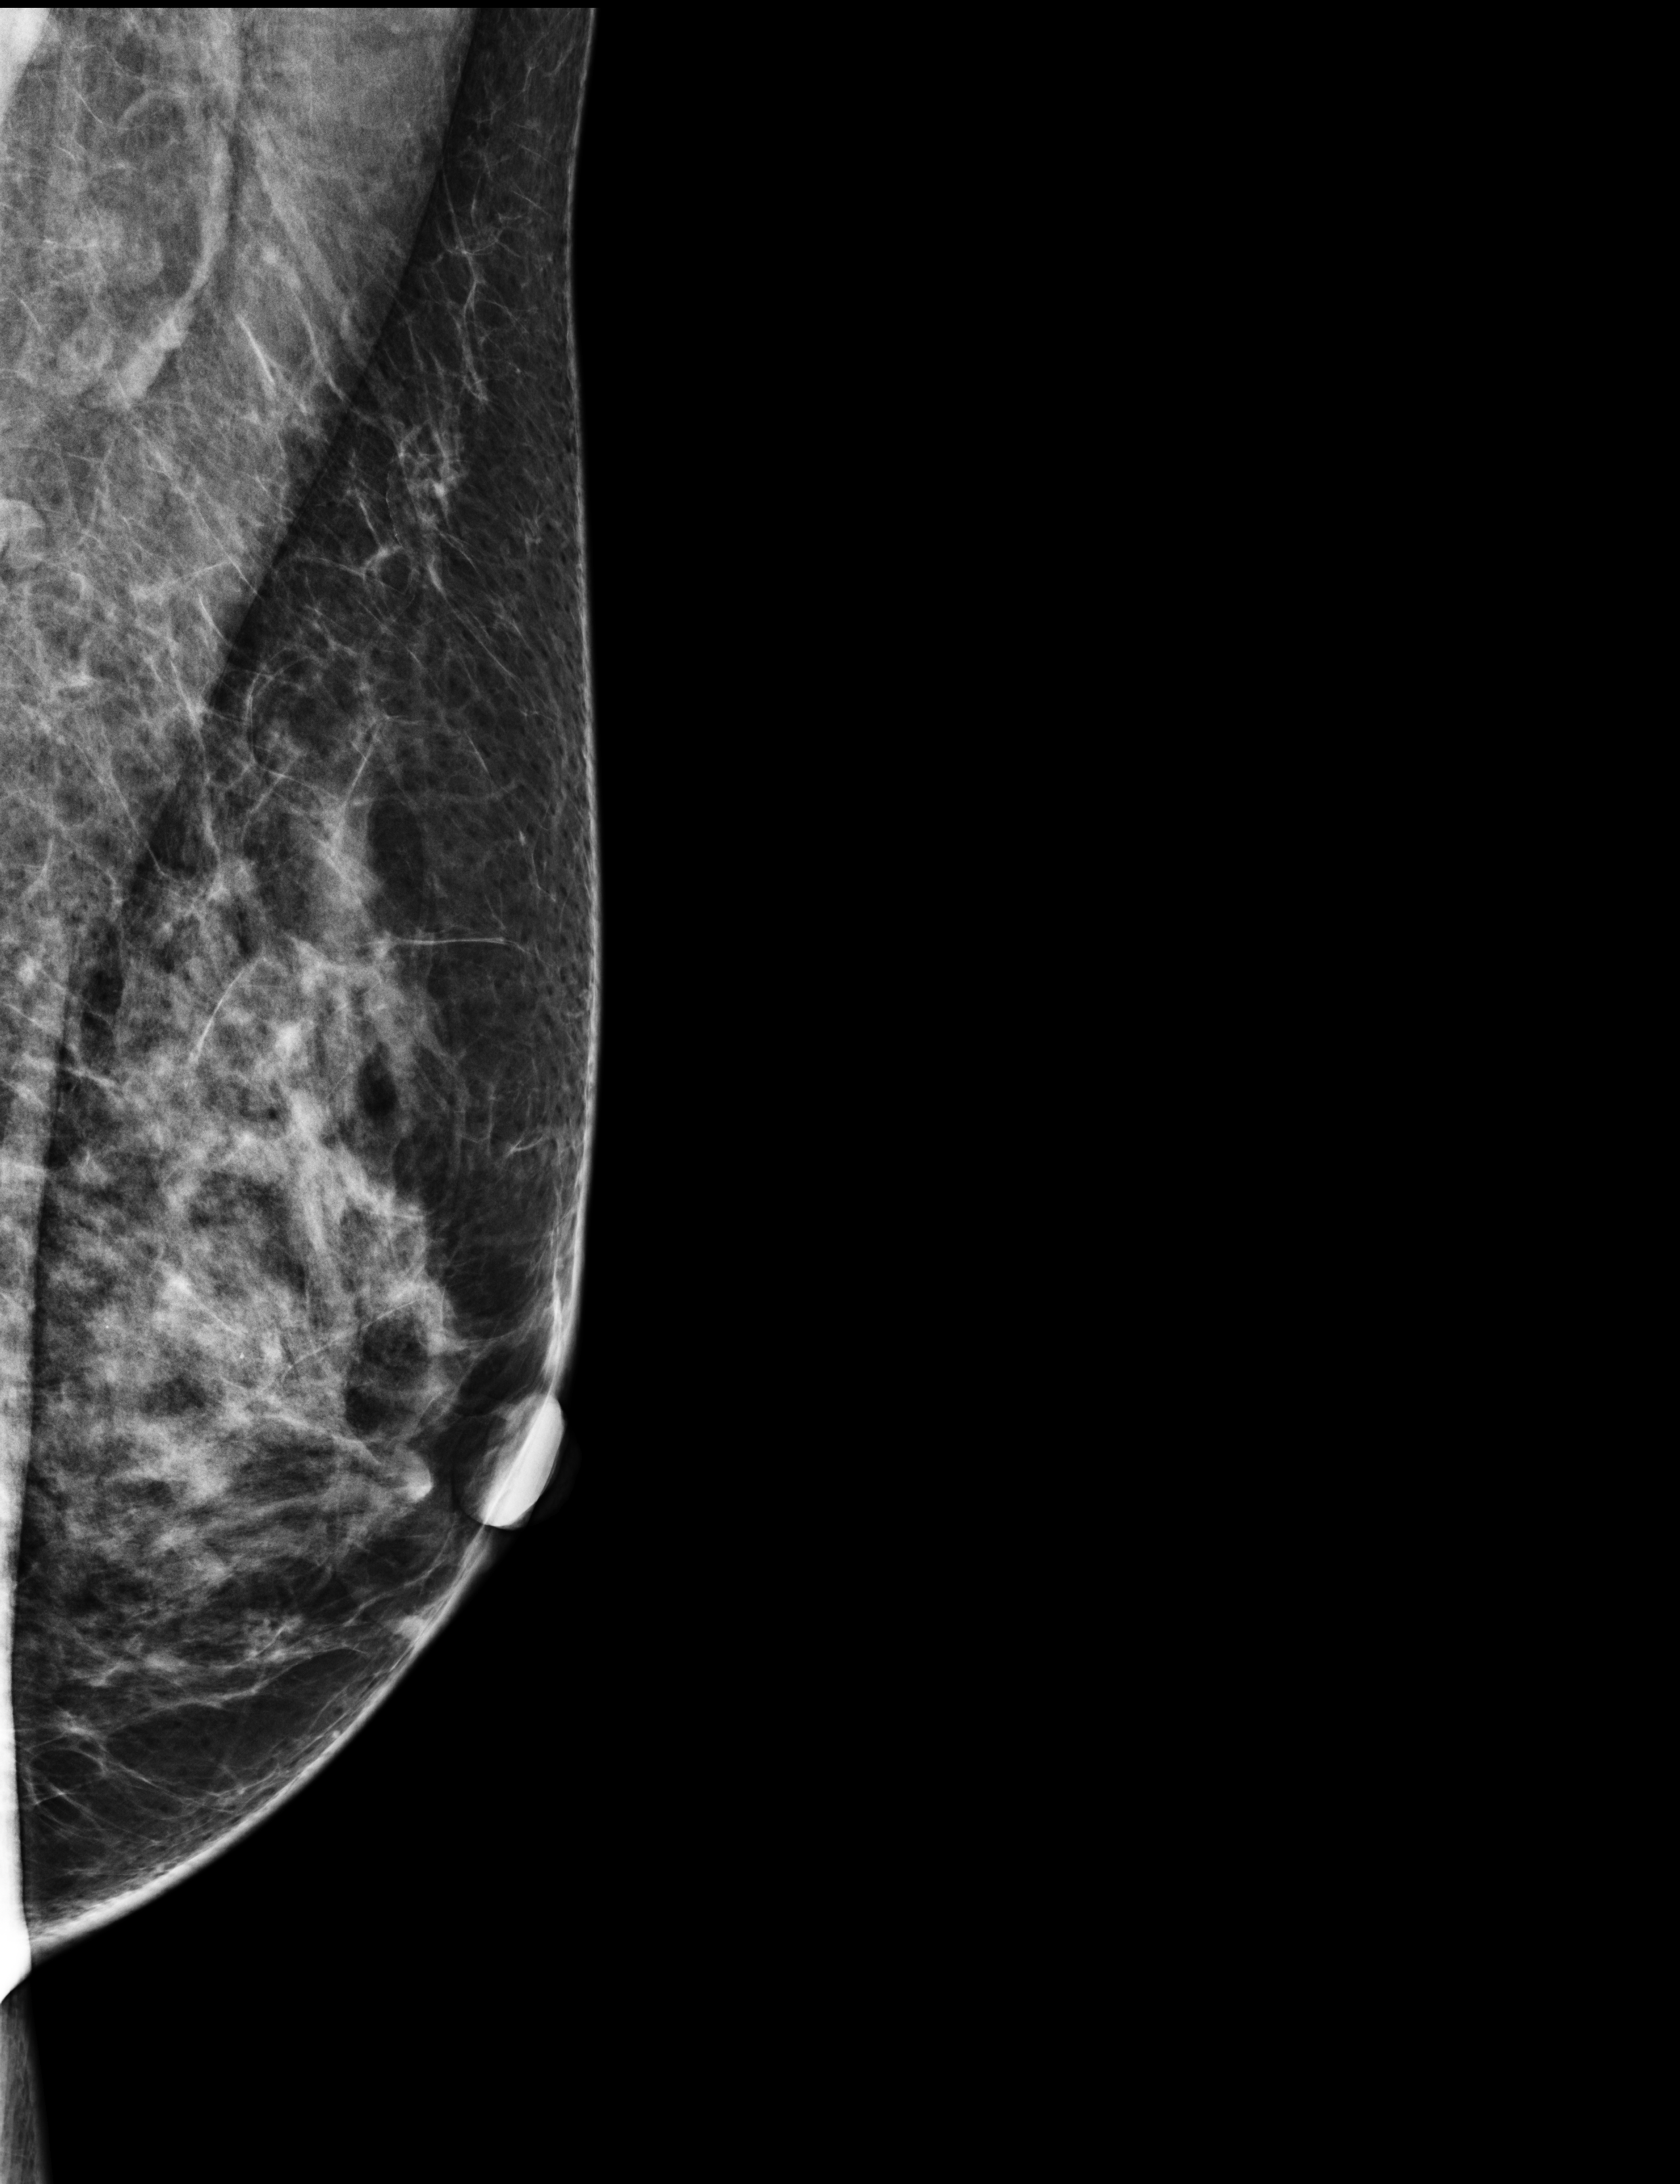
Full-field digital mammogram (FFDM), left breast, medio-lateral oblique projection, annual screening mammography examination. Female patient, age 54 years.
- BI-RADS breast density category at the screening exam (both breasts, scale 1–4): 3
- final BI-RADS assessment for this screening round (tomosynthesis exam, both breasts): category 1
- recall: no recall after this screen